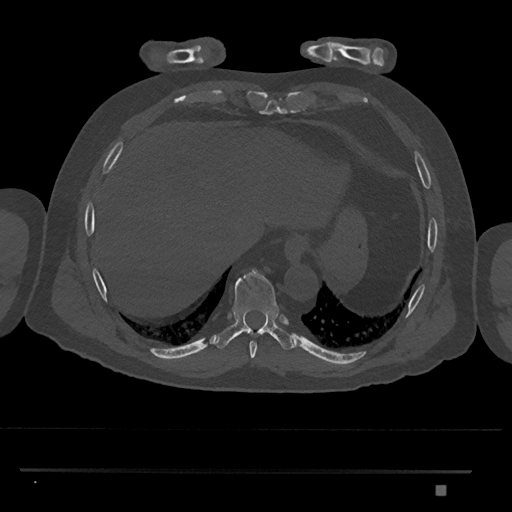
CT including the spine, one axial slice; slice 1070 of 1134 in the series (ordered by position); reconstruction kernel Br40s/3; 120 kVp; bone window (W 1800 / L 400 HU); 0.5 mm slice thickness; 512 × 512 image matrix. Male patient, age 65 years. From the clinical record (not read from this slice): primary cancer: prostate.
Structures marked on this image (semi-automatic segmentation, software-assisted and operator-edited):
- T8 vertebra: bounding box [x1, y1, x2, y2] px = [250, 341, 257, 360]
- T9 vertebra: [215, 269, 294, 350]